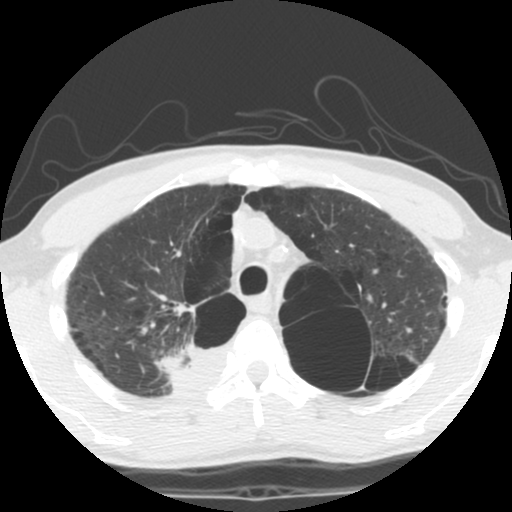
Low-dose screening chest CT, one axial slice. Position 89 of 119 along the scan axis. 140 kVp. Lung window (W 1500 / L -600 HU). 2.5 mm slice thickness. 512 × 512 image matrix, field of view 295 × 295 mm.
Annotated regions visible in this slice (manually delineated by an expert):
- lesion 1 (tumor, upper lobe of right lung): box from (x=161, y=343) to (x=231, y=393) px